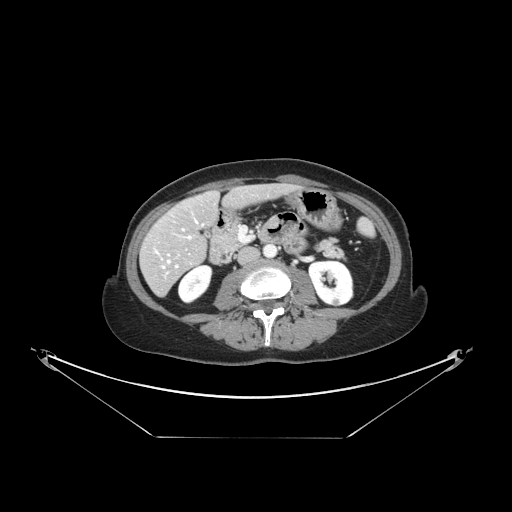
Contrast-enhanced abdominal CT, one axial slice; position 50 of 148 along the scan axis; intravenous contrast given; soft-tissue window (W 400 / L 40 HU); 2.5 mm slice thickness; 512 × 512 image matrix, field of view 500 × 500 mm. Female patient, age 73 years. From the clinical record (not read from this slice): diagnosis: colorectal cancer liver metastases, imaged before liver resection; multiple liver metastases: no; largest metastasis: 1 cm; chemotherapy before resection: yes.
Outlined on this slice (expert manual segmentation):
- hepatic veins: box from (x=156, y=220) to (x=198, y=268) px
- liver: (x=143, y=185)–(x=290, y=295)
- planned liver remnant (the part of the liver to remain after resection): (x=162, y=185)–(x=290, y=247)